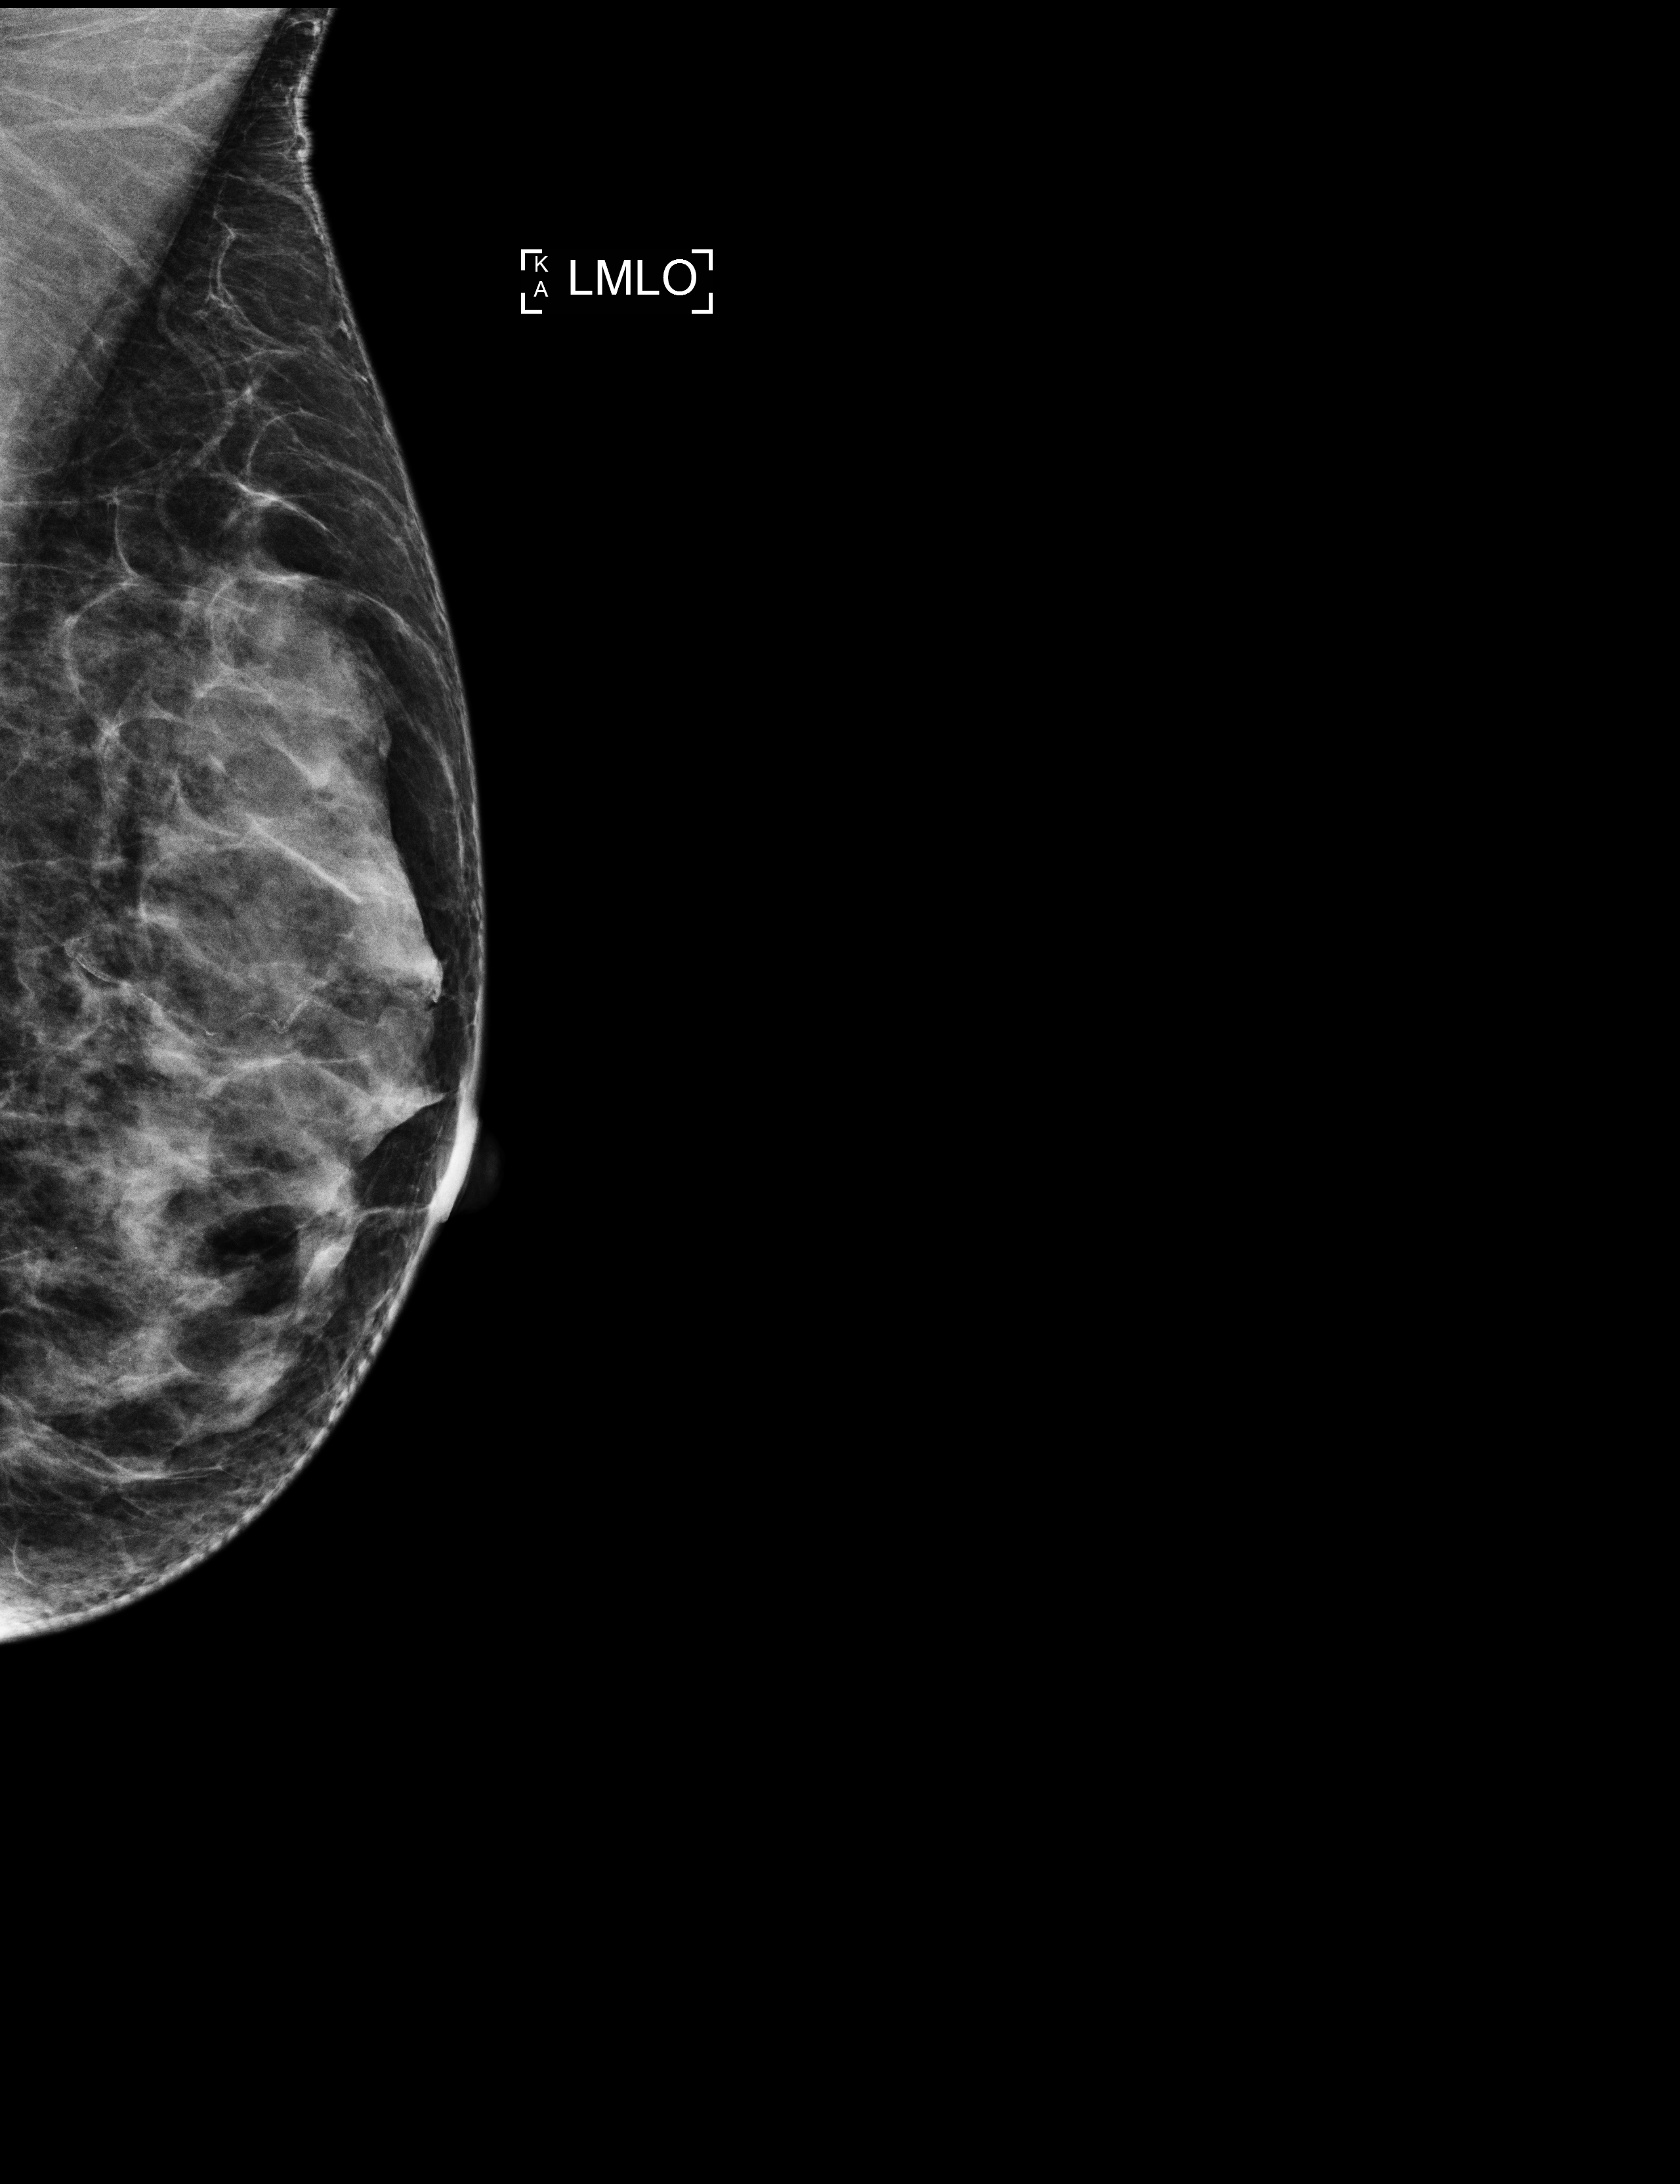
Screening examination, compressed breast thickness 36 mm, system: Selenia Dimensions. Female patient, age 59 years.
Image type: full-field digital mammogram. Breast: left. Projection: mediolateral oblique (MLO) view.